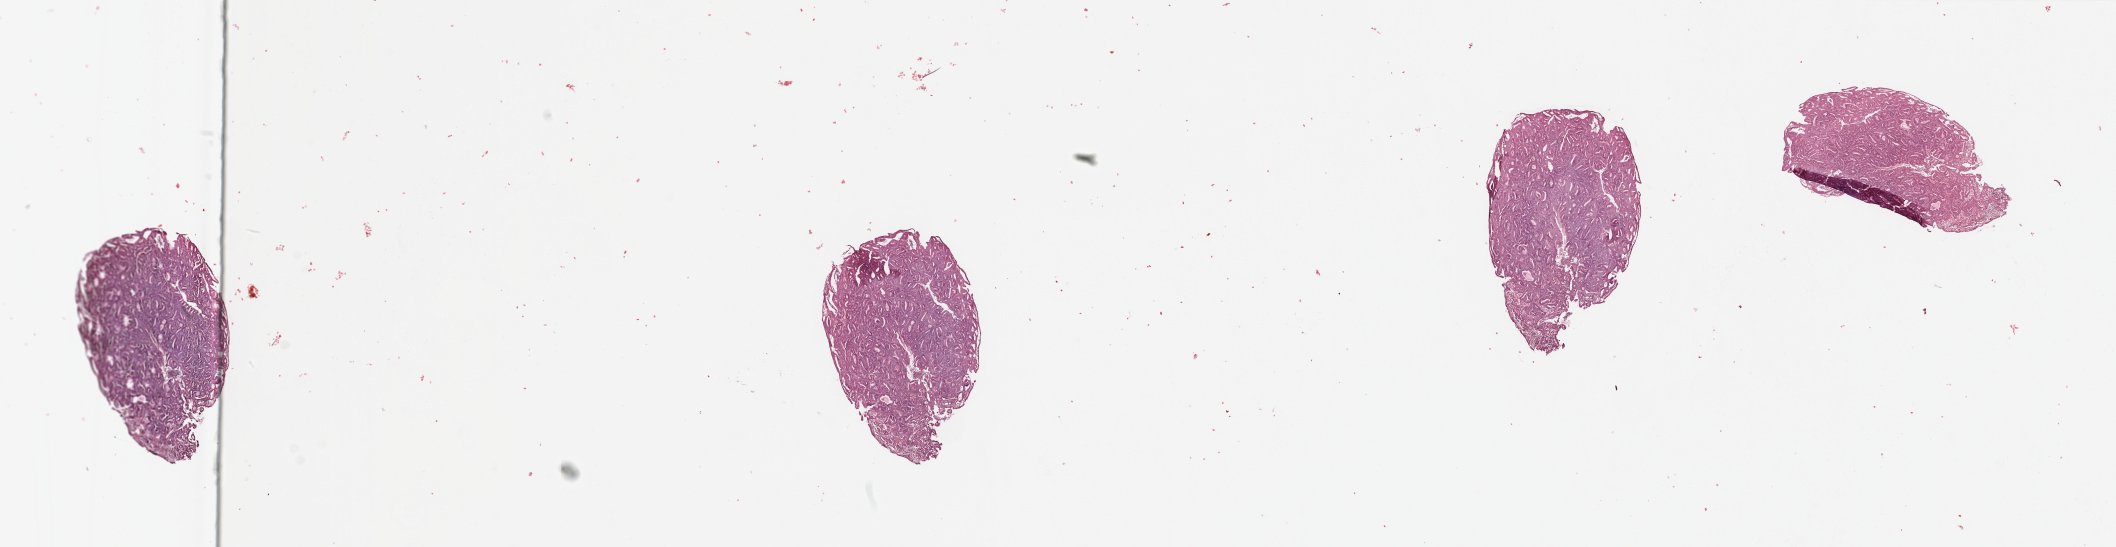
Whole-slide histology image, Hematoxylin and eosin (H&E) stained — low-resolution overview of the scanned area, about 33.5 x 8.7 mm (acquisition: 20x scan); tumour tissue sample, sampled site: uterus. Female, 59 y/o. Histologic grade: G2 (moderately differentiated). Pathologist review of this section (percent, as recorded): tumour nuclei 90%, necrosis 0%.
* primary tumour site (as recorded): anterior endometrium
* diagnosis: Endometrioid adenocarcinoma, NOS
* AJCC pathologic stage: I